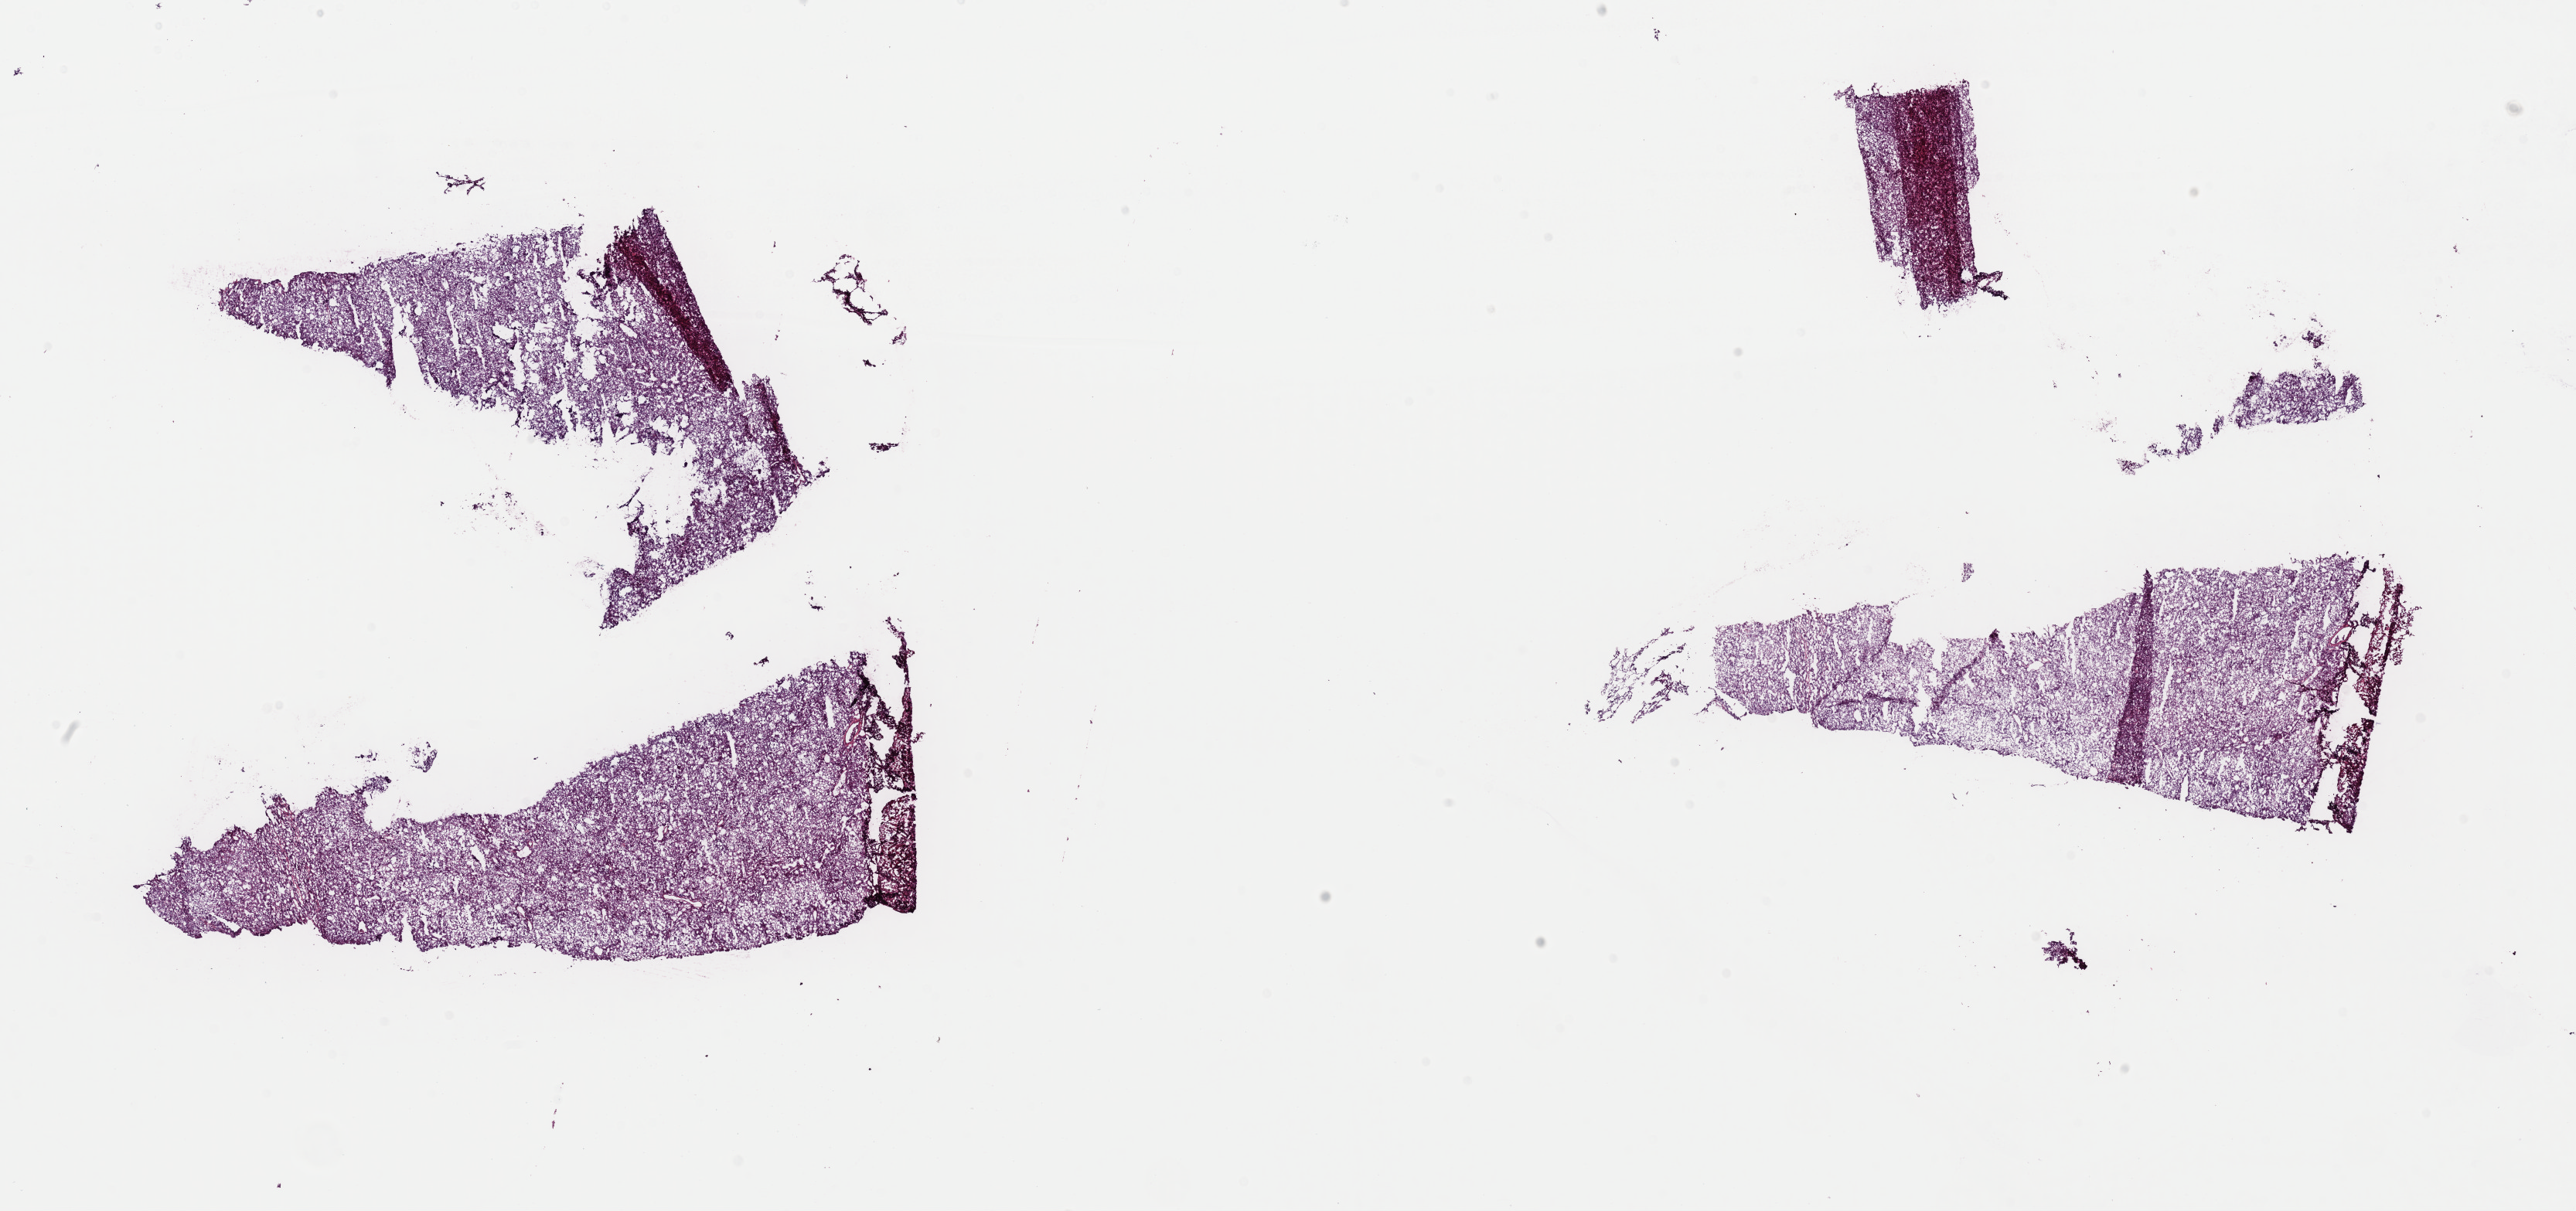
H&E-stained whole-slide image — low-resolution overview of the scanned area, about 26.3 x 12.4 mm (slide scanned at 40x). Frozen section. Sample: primary tumour, liver. Patient: male, age at initial diagnosis 58 years. Histologic grade: G1 (well differentiated). Slide review estimates, as recorded: tumour cells 70%, tumour nuclei 80%, normal cells 0%, stromal cells 20%, necrosis 10%. Infiltration values recorded for this section: lymphocyte infiltration 0%, monocyte infiltration 0%, neutrophil infiltration 0%.
Histologic diagnosis: Hepatocellular carcinoma, NOS. AJCC pathologic stage: I (7th edition).